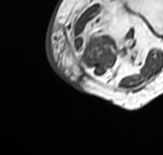
MRI of an extremity soft-tissue mass, one axial slice; slice 3 of 65 in the series (ordered by position); MR volume resampled by the dataset authors to the PET/CT grid (not the native acquisition matrix); 3.27 mm slice thickness; 163 × 155 image matrix, field of view 159 × 151 mm. Female patient. Case-level facts recorded for this patient, not image findings: histological type: pleomorphic leiomyosarcoma; grade: high; site of the primary tumour: left thigh.
Structures marked on this image (expert contour drawn on MRI and transferred to this co-registered scan by the dataset authors):
- gross tumour volume including surrounding oedema: bounding box [x1, y1, x2, y2] px = [69, 1, 143, 77]